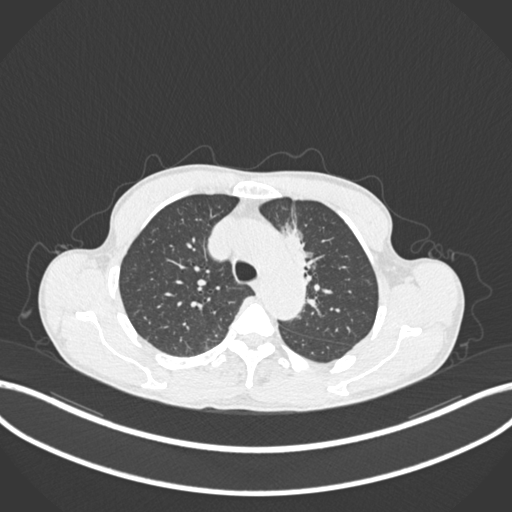
Chest CT, one axial slice; position 148 of 211 along the scan axis; reconstruction kernel B30f; 120 kVp; lung window (W 1500 / L -600 HU); 512 × 512 image matrix, field of view 400 × 400 mm. Patient: male, 58 years. From the clinical record (not read from this slice): clinical TNM (as recorded): T1c N1 M0.
Annotated regions visible in this slice (rectangle marked by the reading radiologist):
- lung tumour (recorded histology: adenocarcinoma): bounding box [x1, y1, x2, y2] px = [275, 211, 323, 289]